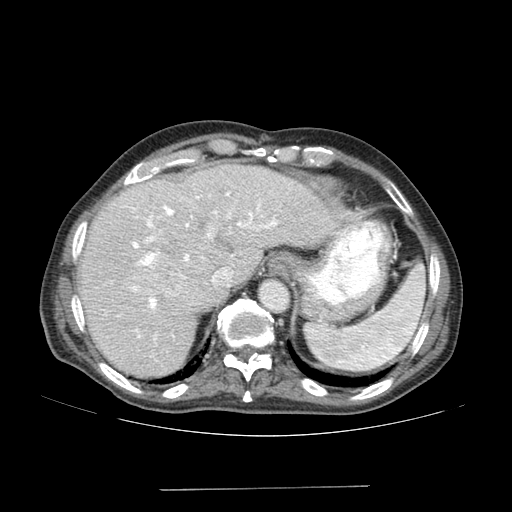
Contrast-enhanced abdominal CT (liver protocol), one axial slice. Position 122 of 192 along the scan axis. Reconstruction kernel SOFT. Soft-tissue window (W 400 / L 40 HU). 2.5 mm slice thickness. 512 × 512 image matrix, field of view 400 × 400 mm. From the clinical record (not read from this slice): diagnosis: hepatocellular carcinoma (patient treated with transarterial chemoembolisation; whether this scan precedes or follows treatment is not stated here); TNM stage (as recorded): Stage-IVA; Child-Pugh class: A; tumour differentiation: poorly differentiated; tumour nodularity: uninodular.
Structures marked on this image (semi-automatically segmented with operator editing):
- liver parenchyma outside the tumour (the mass and vessels are separate outlines, so this box may not span the whole liver): box from (x=78, y=164) to (x=351, y=377) px
- mass: (x=130, y=259)–(x=187, y=297)
- liver vessels: (x=132, y=192)–(x=277, y=340)